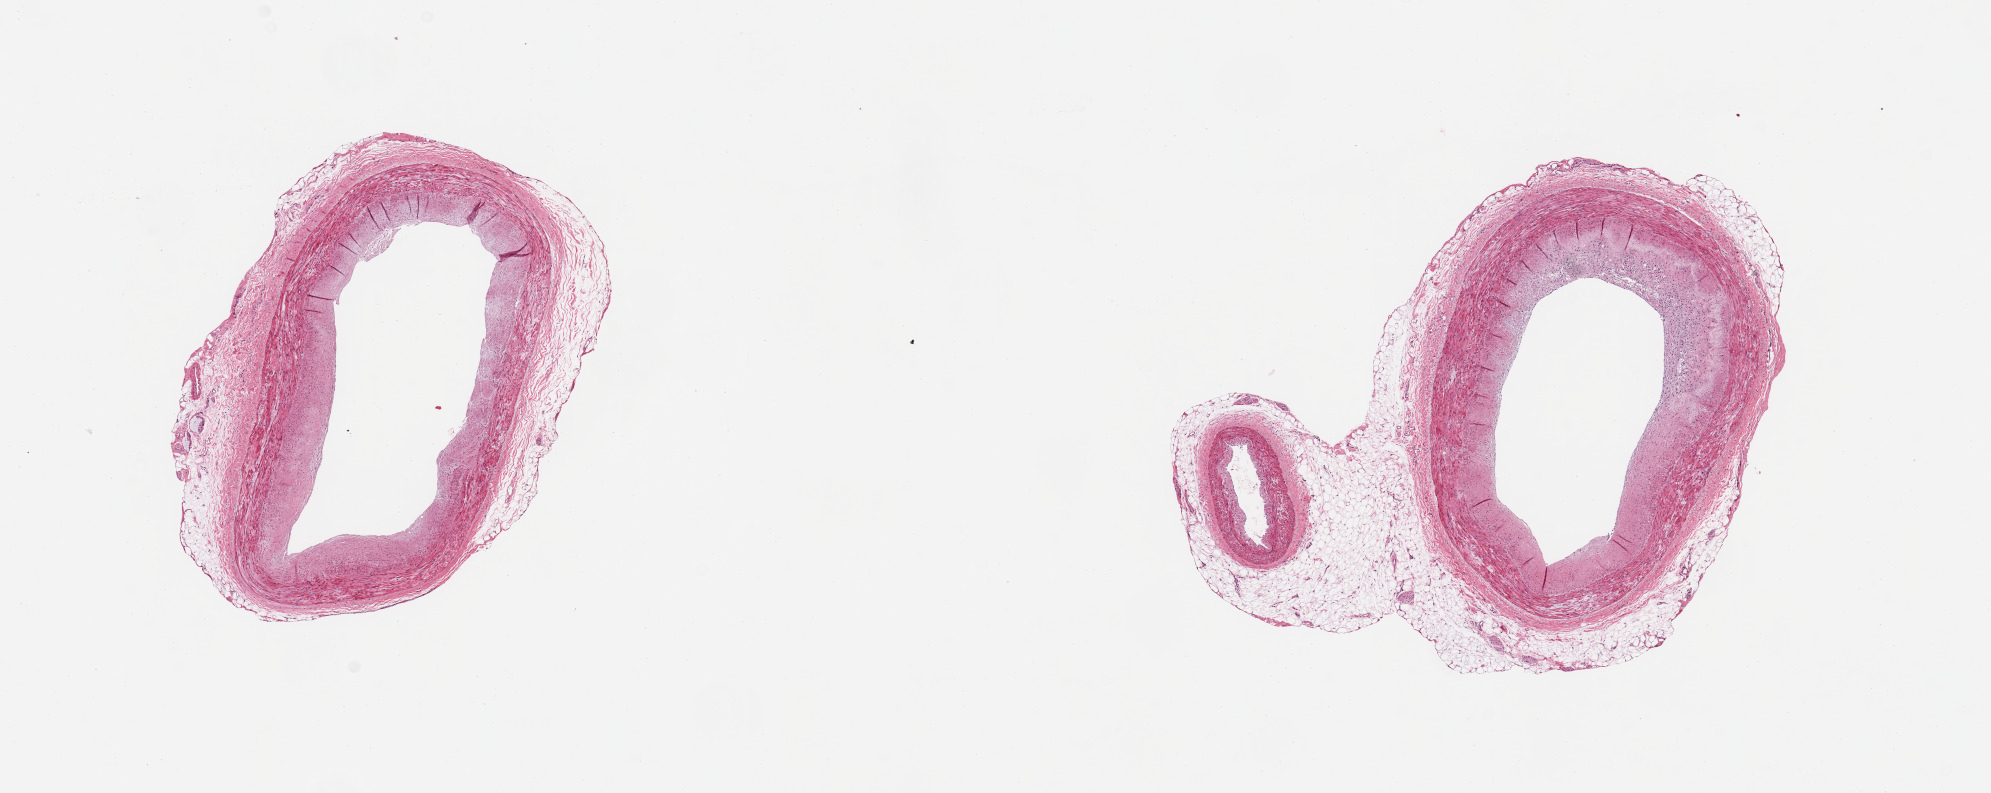
Whole-slide image, haematoxylin and eosin stain, brightfield — shown as a low-resolution overview of the whole scanned area (about 15.8 x 6.3 mm). PAXgene-fixed paraffin-embedded (PFPE) section. Section of coronary artery (target tissue). Donor tissue sample. Female donor.
- reviewer comment on this tissue sample: 2 pieces; patent lumen with atherosclerotic plaque; up to ~2mm adherent adventitia and external fat